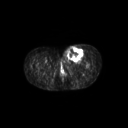
FDG PET of an extremity soft-tissue mass (from a PET/CT study), one axial slice; slice 51 of 267 in the series (ordered by position); 3.27 mm slice thickness; 128 × 128 image matrix, field of view 600 × 600 mm. Female patient, age 24 years. From the clinical record (not read from this slice): histological type: leiomyosarcoma; grade: high; site of the primary tumour: groin.
Outlined on this slice (expert contour drawn on MRI and transferred to this co-registered scan by the dataset authors):
- gross tumour volume including surrounding oedema: bounding box <62,44,84,62> (left, top, right, bottom; pixels)
- gross tumour volume (mass): <67,46,84,60>